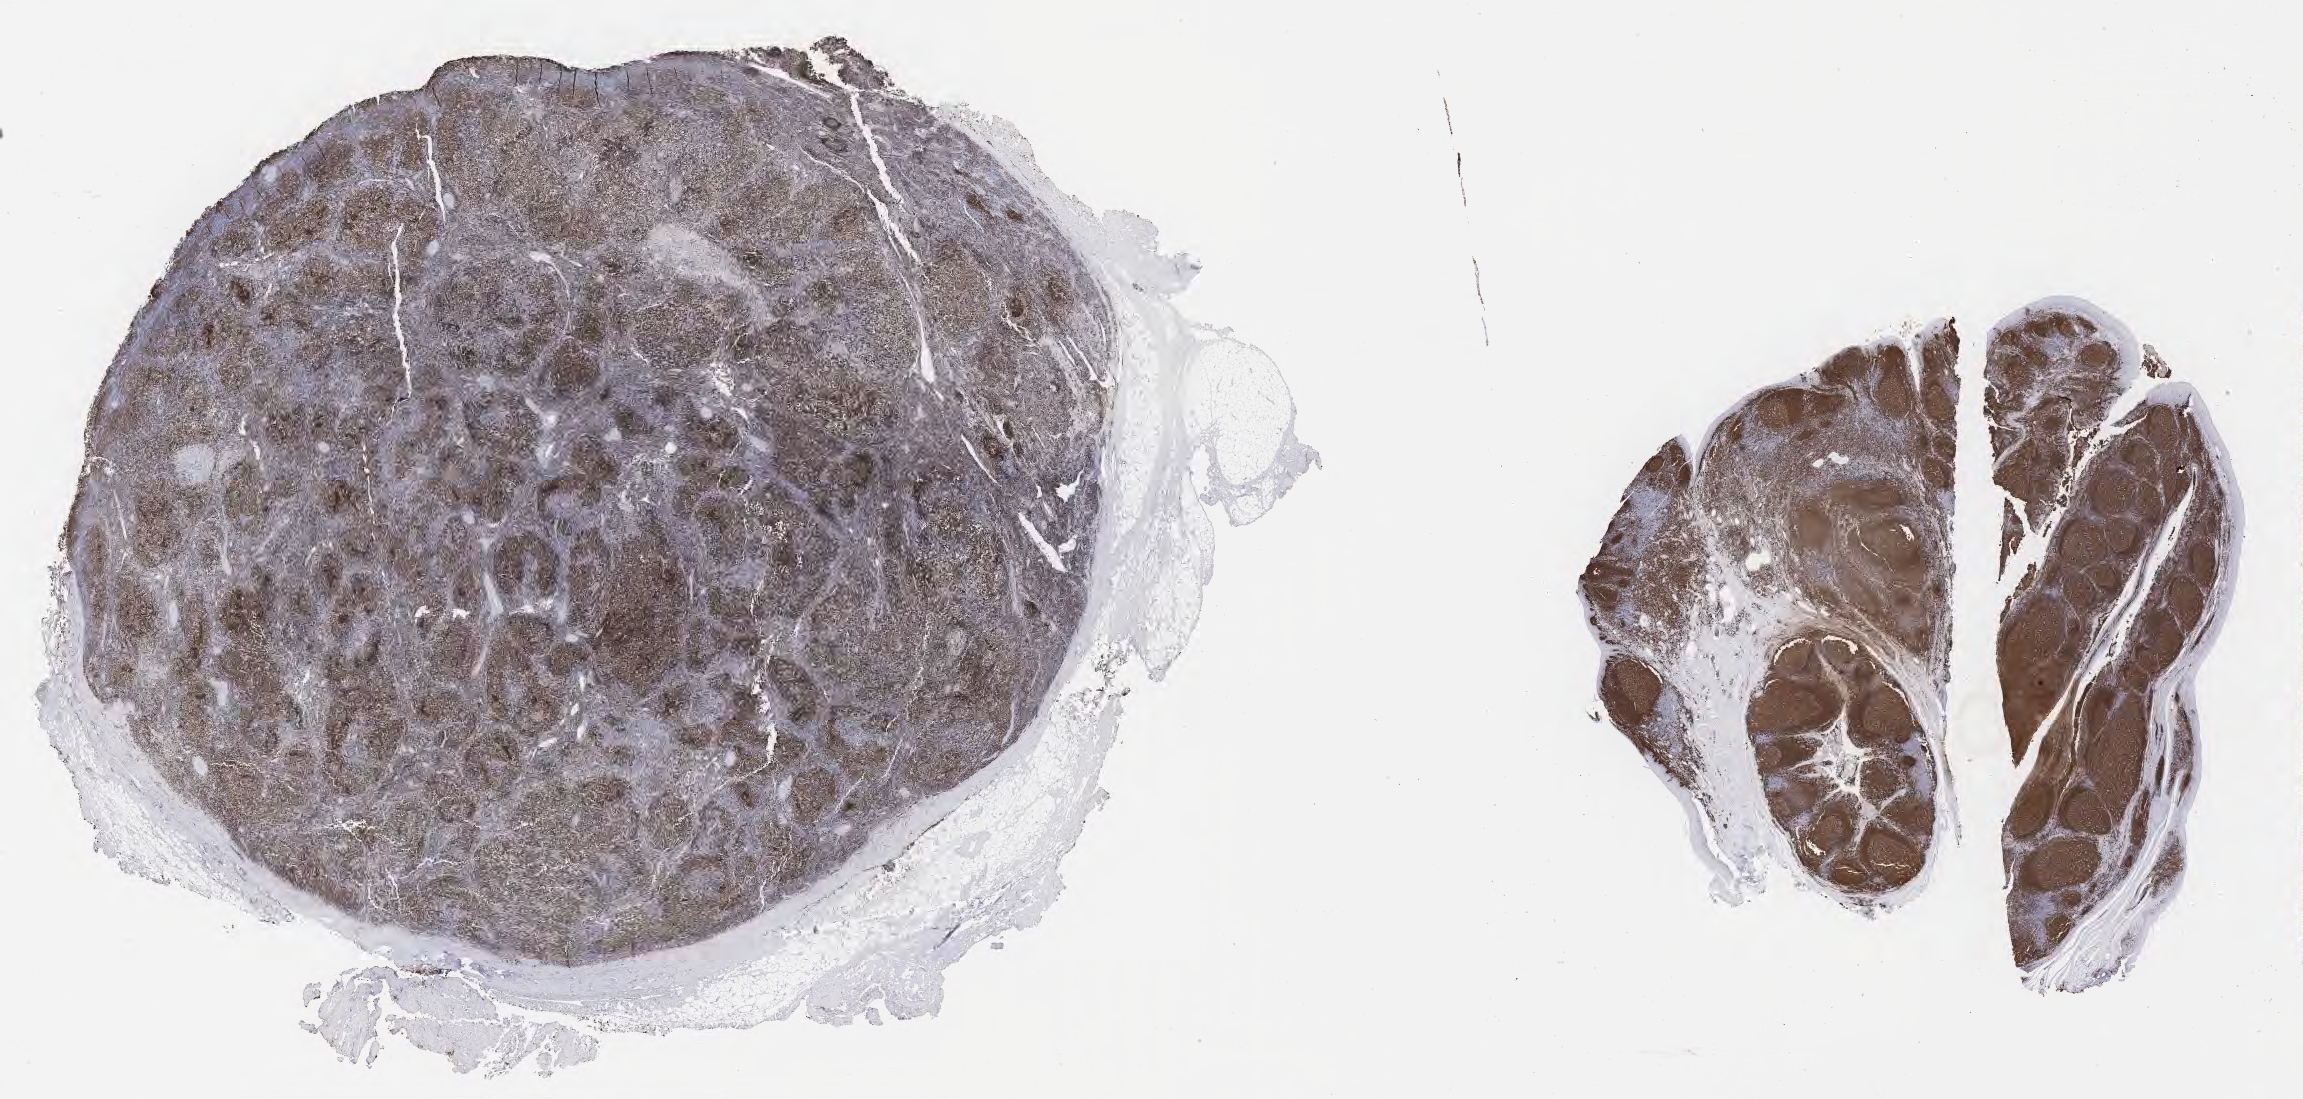
Whole-slide image, immunohistochemical stain for CD79a — a low-resolution overview of the entire scanned area, about 37.2 x 17.8 mm. Tumor tissue. Site: lymph node. Patient male; age 46 years.
Histologic diagnosis: Diffuse large B-cell lymphoma, NOS.